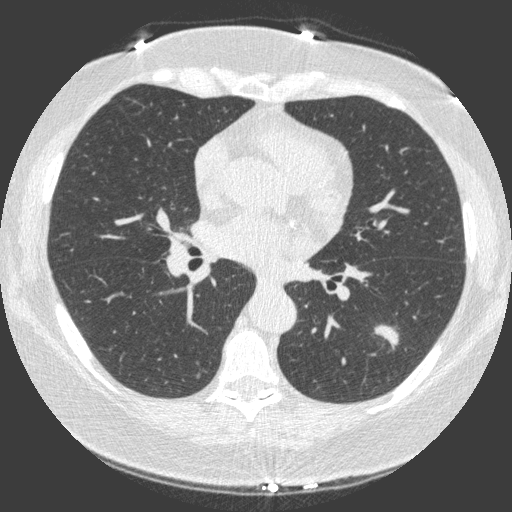
Low-dose screening chest CT, axial slice. Third annual screen. Lung window (W 1500 / L -600 HU). 1 mm slice thickness. Slice 67 of 149 in the series. Female participant, aged 66 years at enrolment.
• Expert-annotated lung lesion, bounding box (x1, y1, x2, y2) in pixels: (361, 303, 419, 357).
• Screening reader's record for this exam (one nodule recorded; not confirmed to be the boxed lesion): non-calcified nodule or mass ≥4 mm, left lower lobe, 23 × 17 mm, spiculated (stellate) margins, soft tissue attenuation, pre-existing on the prior screen: yes; interval growth: yes.
• Official screen result: positive, other.
• Participant outcome: lung cancer diagnosed 15 days after this screen — non-small cell carcinoma, left lower lobe, poorly differentiated (G3), stage IA (AJCC 6th edition), 20 mm at pathology.